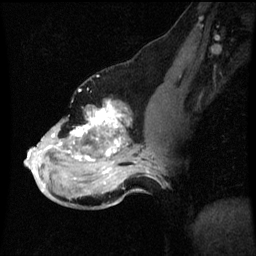
Breast MRI (dynamic contrast-enhanced), one sagittal slice. Position 32 of 60 along the scan axis. Dynamic contrast-enhanced series, image 2 of 3 at this slice position (ordered by acquisition). 1.5 T. TE 4.2 ms, TR 8.9 ms. 2 mm slice thickness. 256 × 256 image matrix, field of view 200 × 200 mm. Female patient, age 49 years. Case-level facts recorded for this patient, not image findings: setting: breast cancer imaged before/during neoadjuvant chemotherapy; receptor status: HR-positive, HER2-negative.
Annotated regions visible in this slice (semi-automatically segmented with operator editing):
- analysis volume of interest (the breast-tissue region the enhancement analysis was run in; not a lesion): bounding box [x1, y1, x2, y2] px = [26, 102, 159, 199]
- tumour enhancement mask (voxels above the 70 % enhancement threshold inside the analysis volume of interest): [28, 102, 149, 187]